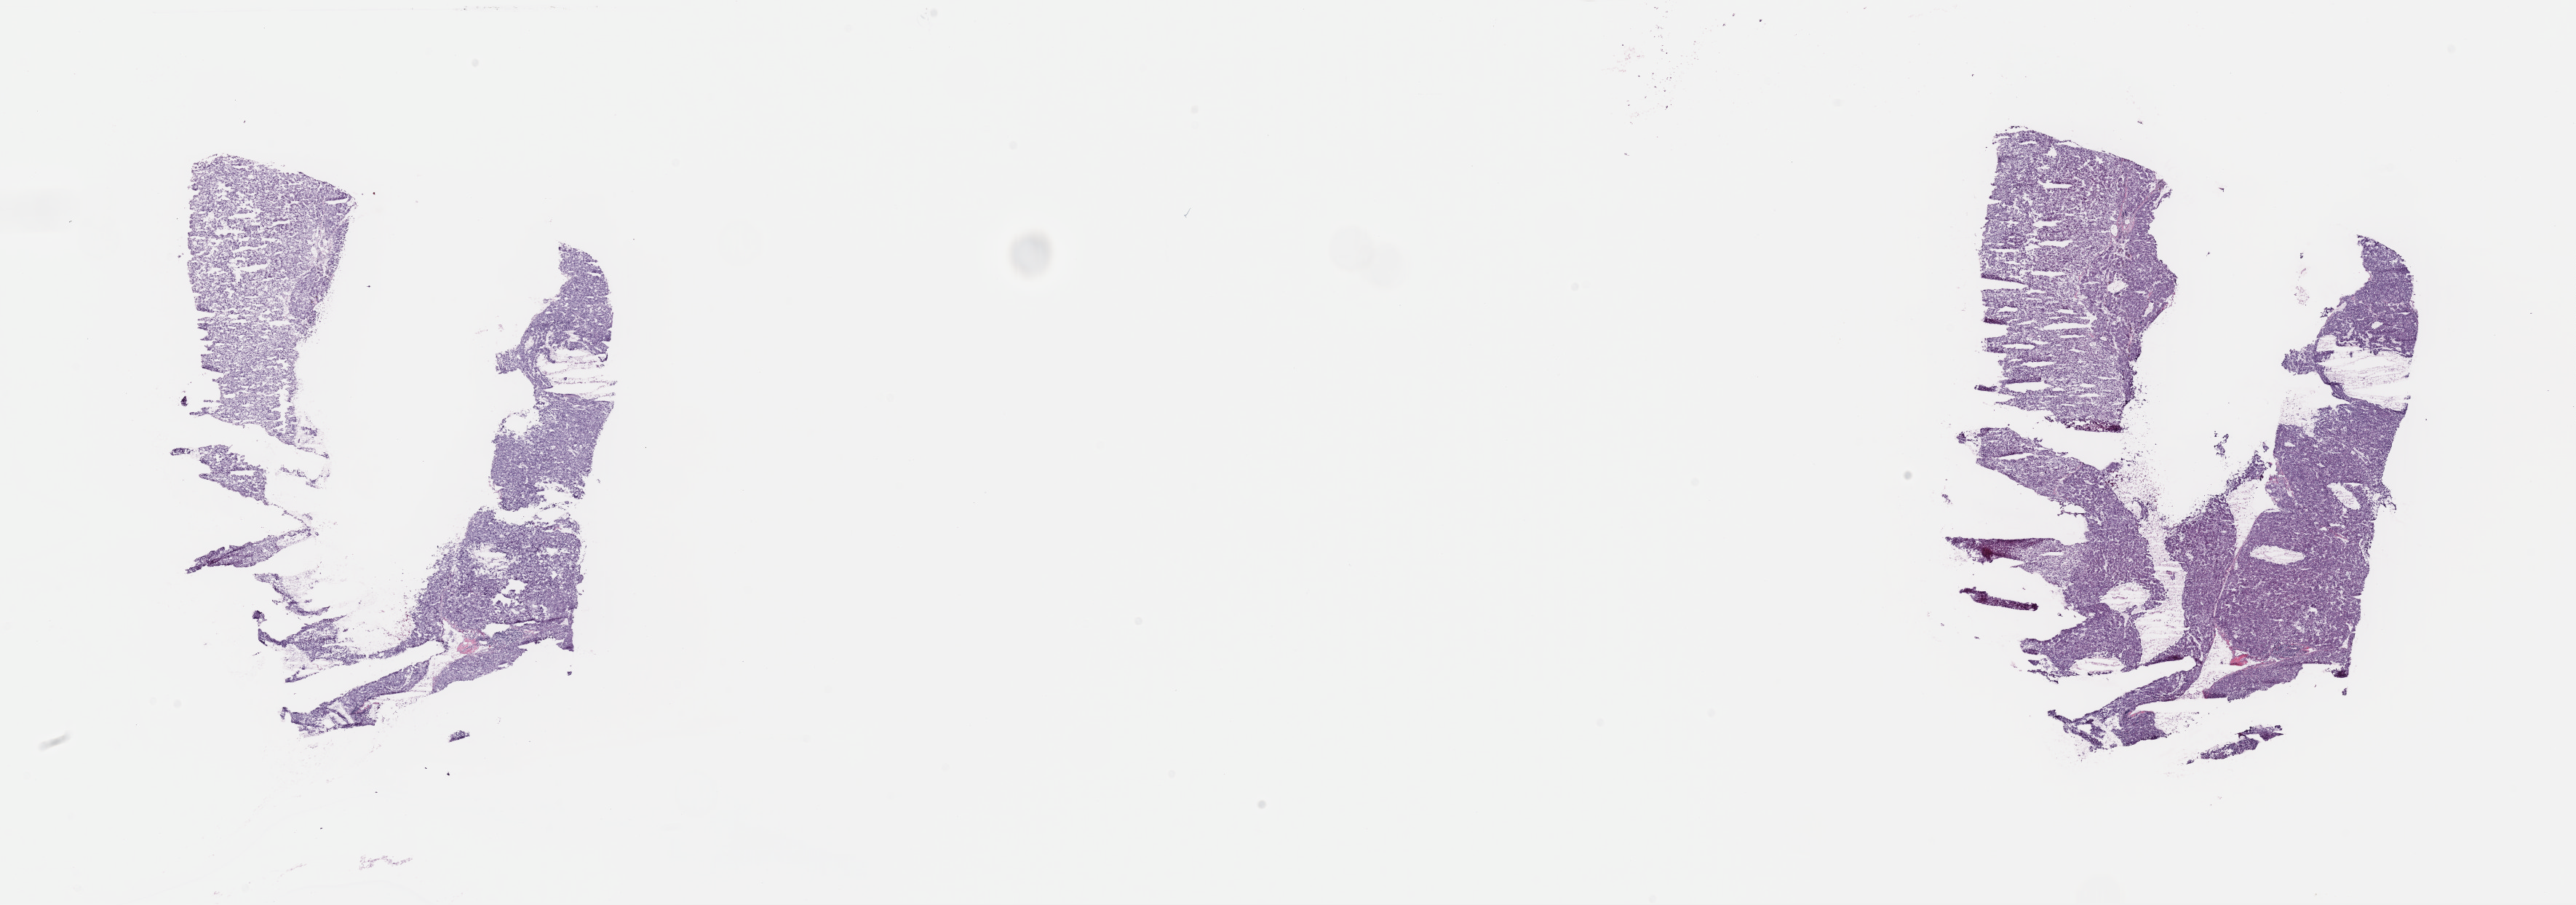
H&E-stained whole-slide image, low-resolution overview of the scanned area, about 28.0 x 9.8 mm (acquisition: 40x scan). Frozen section from the top of the tissue portion. Liver, primary tumour sample. Patient: female, age at initial diagnosis 29 years. Histologic grade: G2 (moderately differentiated). Slide review estimates, as recorded: tumour cells 75%, tumour nuclei 75%, normal cells 20%, stromal cells 5%, necrosis 0%. Inflammatory infiltration, as recorded: lymphocyte infiltration 1%, monocyte infiltration 0%, neutrophil infiltration 0%.
- AJCC pathologic stage: III (4th edition)
- pathologic diagnosis: Hepatocellular carcinoma, NOS